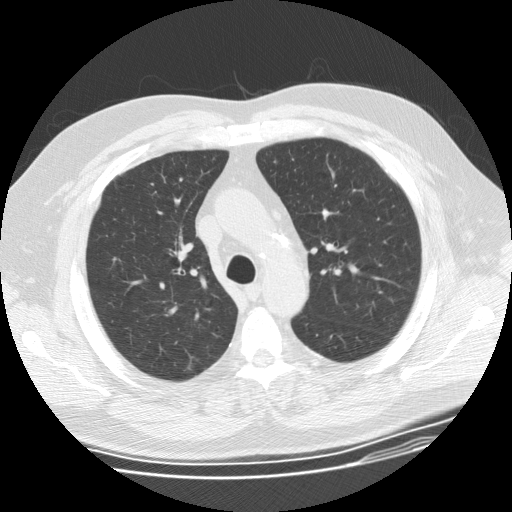
Low-dose screening chest CT, one axial slice; position 108 of 155 along the scan axis; 120 kVp; lung window (W 1500 / L -600 HU); 512 × 512 image matrix.
Outlined on this slice (manually delineated by an expert):
- lesion 1 (tumor, upper lobe of right lung): bounding box [x1, y1, x2, y2] px = [183, 355, 194, 374]